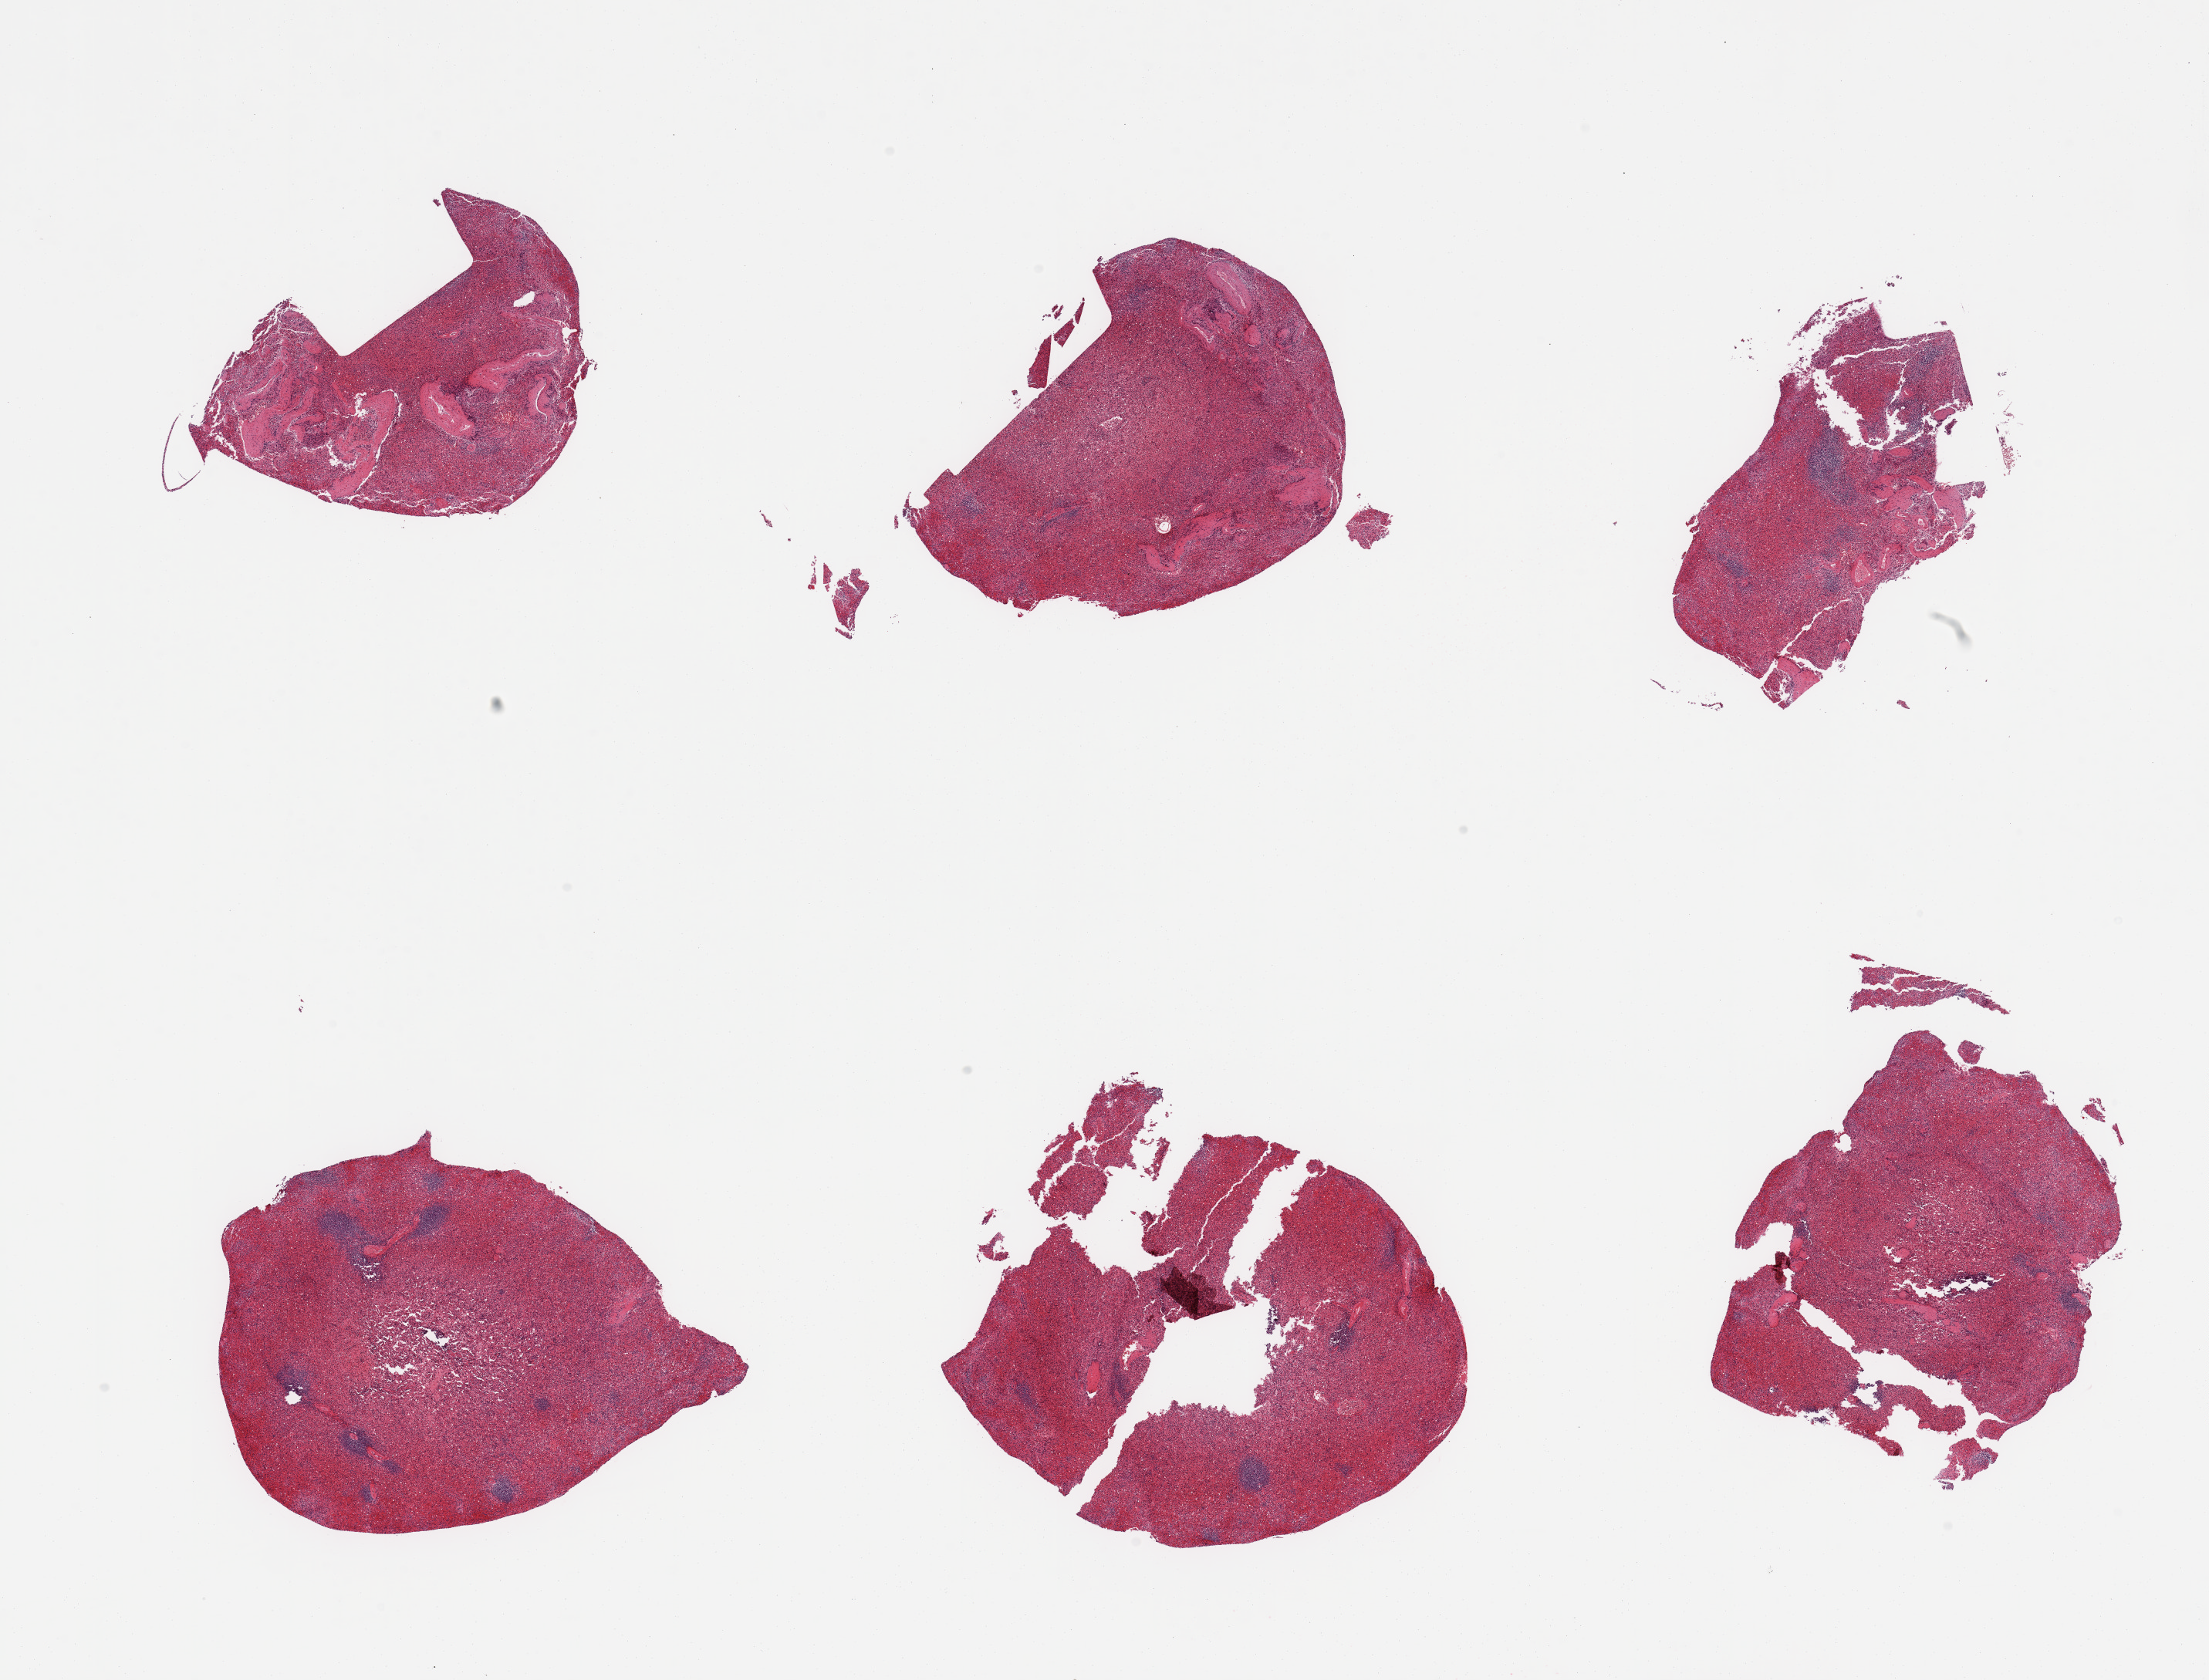
Haematoxylin and eosin whole-slide image, shown as a low-resolution overview of the whole scanned area (about 22.6 x 17.2 mm), PAXgene-fixed, paraffin-embedded tissue, sampled site (target tissue): spleen, tissue donor sample. Female donor.
* reviewer comment on this tissue sample: 2 pieces; SPLEEN not kidney